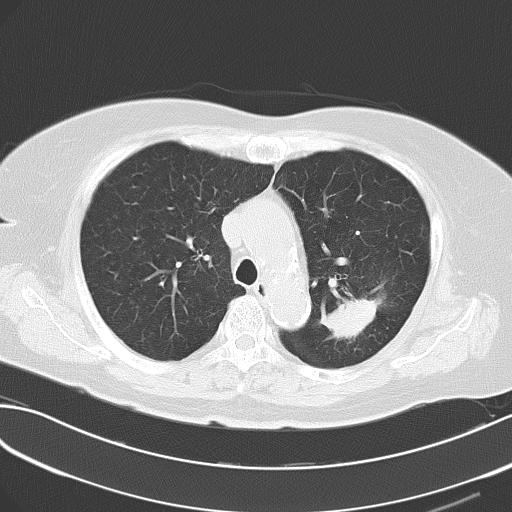
Chest CT, one axial slice; slice 49 of 62 in the series (ordered by position); 120 kVp; lung window (W 1500 / L -600 HU); 5 mm slice thickness; 512 × 512 image matrix, field of view 353 × 353 mm. Female patient, age 70 years. From the clinical record (not read from this slice): clinical TNM (as recorded): T2 N0 M0.
Outlined on this slice (bounding box drawn by a radiologist):
- lung tumour (recorded histology: adenocarcinoma): box from (x=319, y=287) to (x=384, y=345) px